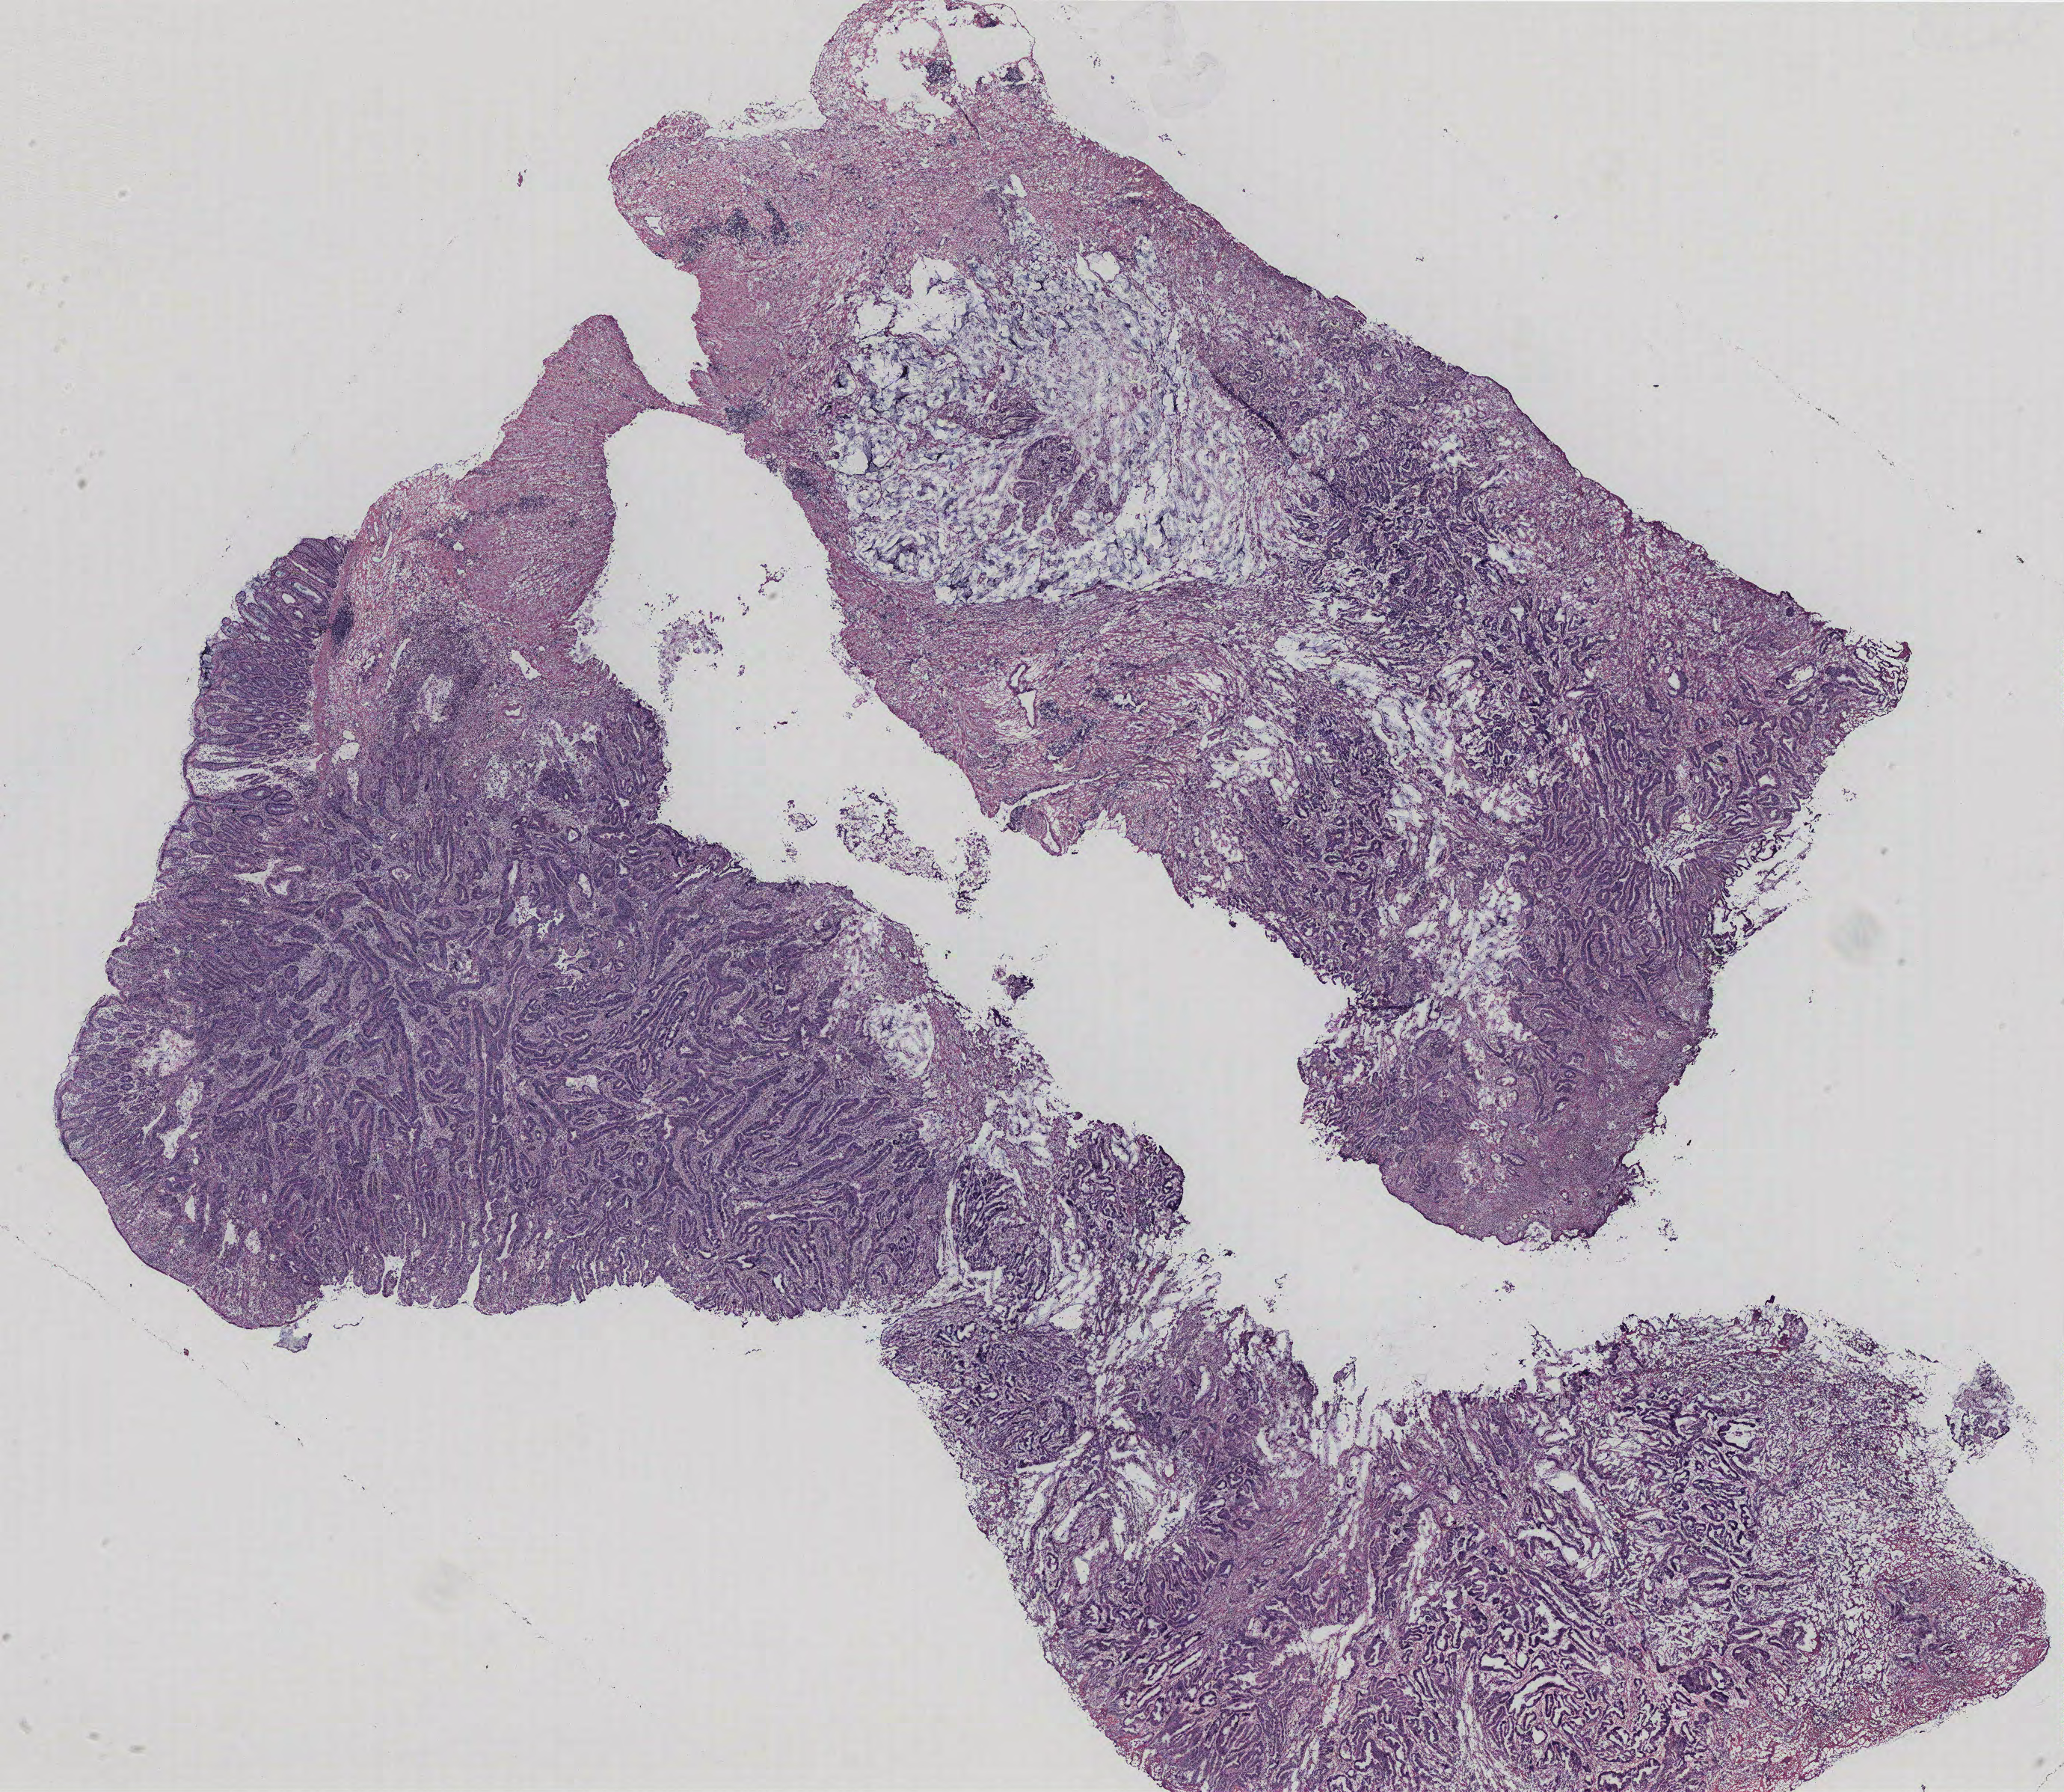
Whole-slide histology image, H&E — shown as a low-resolution overview of the whole scanned area (about 22.1 x 19.2 mm, slide scanned at 40x). Colon, tumour tissue. 54-year-old male patient.
AJCC pathologic stage: IIA. Diagnosis: Adenocarcinoma, NOS. Primary tumour site (as recorded): colon.